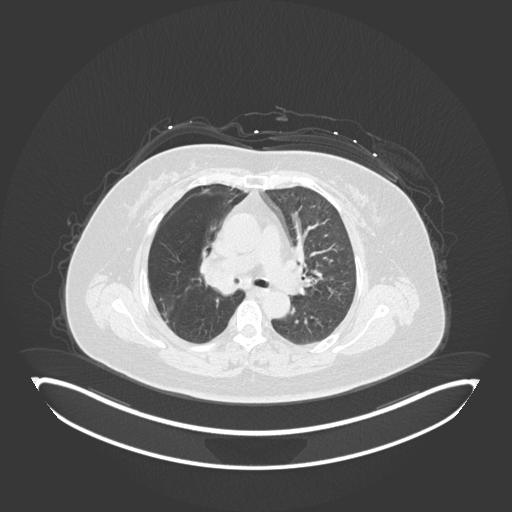
Chest CT, one axial slice; position 106 of 245 along the scan axis; 120 kVp; lung window (W 1500 / L -600 HU); 1 mm slice thickness; 512 × 512 image matrix, field of view 500 × 500 mm. Female patient, age 60 years. Case-level facts recorded for this patient, not image findings: clinical TNM (as recorded): T1c N0 M0.
Annotated regions visible in this slice (rectangle marked by the reading radiologist):
- lung tumour (recorded histology: squamous cell carcinoma): bounding box <197,253,241,298> (left, top, right, bottom; pixels)